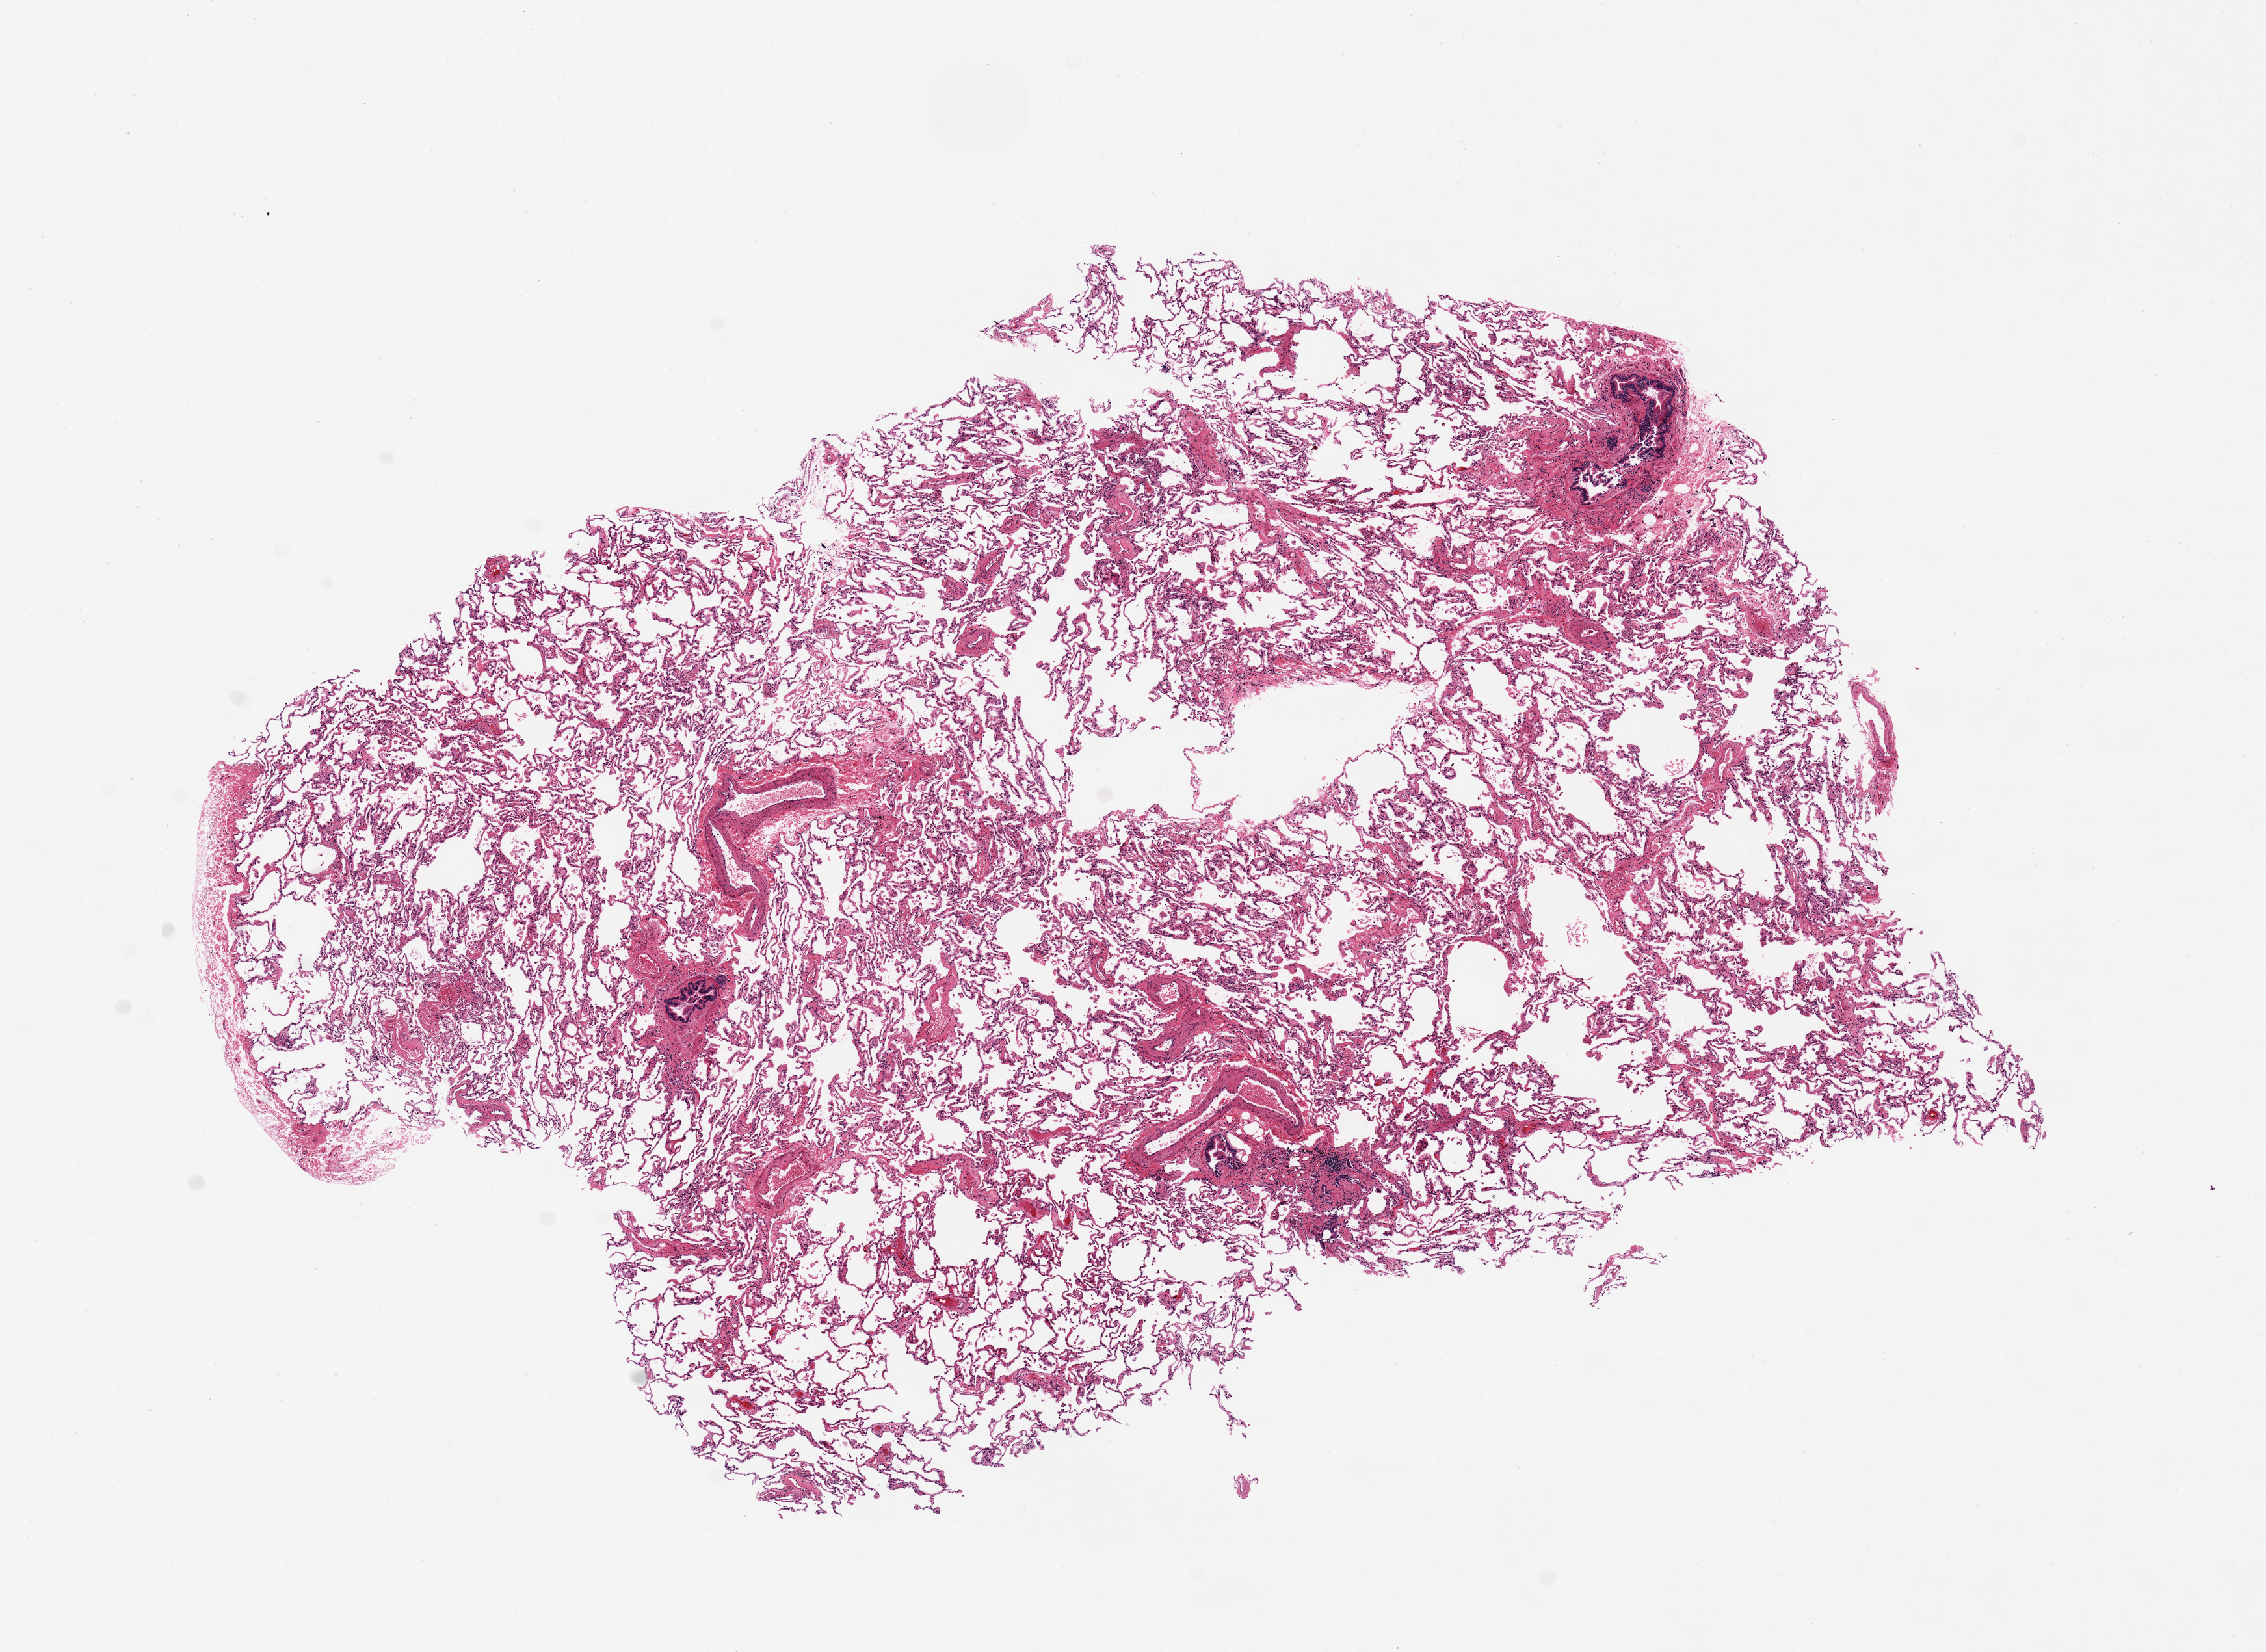
Whole-slide image, haematoxylin and eosin stain, whole scanned area (about 13.8 x 10.0 mm) shown as a low-resolution overview. PAXgene-fixed, paraffin-embedded tissue. Target tissue: lung. Tissue donor sample. Donor: male.
Reviewer comment on this tissue sample: bronchial mucosal sloughing, early. No significant inflammation; clean specimen.